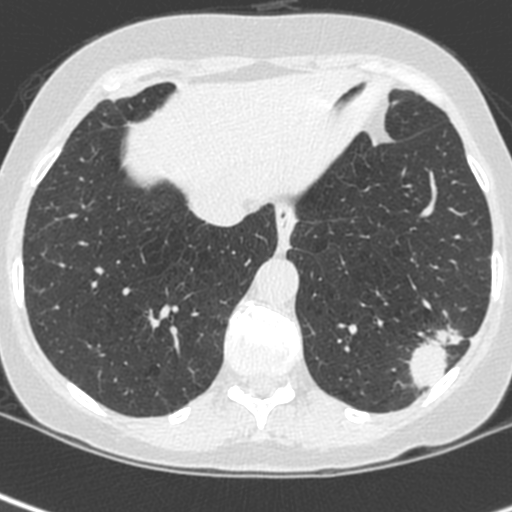
Axial slice from a low-dose chest CT screening exam, baseline screening round, lung window (W 1500 / L -600 HU), 1.3 mm slice thickness, 120 kVp, slice 180 of 252 in the series, 512 × 512 image matrix, field of view 271 × 271 mm. Female participant, aged 56 years at enrolment. Current smoker at enrolment.
Expert reader's lesion annotation, bounding box [x1, y1, x2, y2] px = [401, 306, 480, 387]. Screening reader's record for this exam (one nodule recorded; not confirmed to be the boxed lesion): non-calcified nodule or mass ≥4 mm, left lower lobe, 37 × 29 mm, spiculated (stellate) margins, ground glass attenuation. Later outcome: lung cancer diagnosed 91 days after this screen — squamous cell carcinoma, NOS, left lower lobe, poorly differentiated (G3), stage IIIA (AJCC 6th edition), 35 mm at pathology.